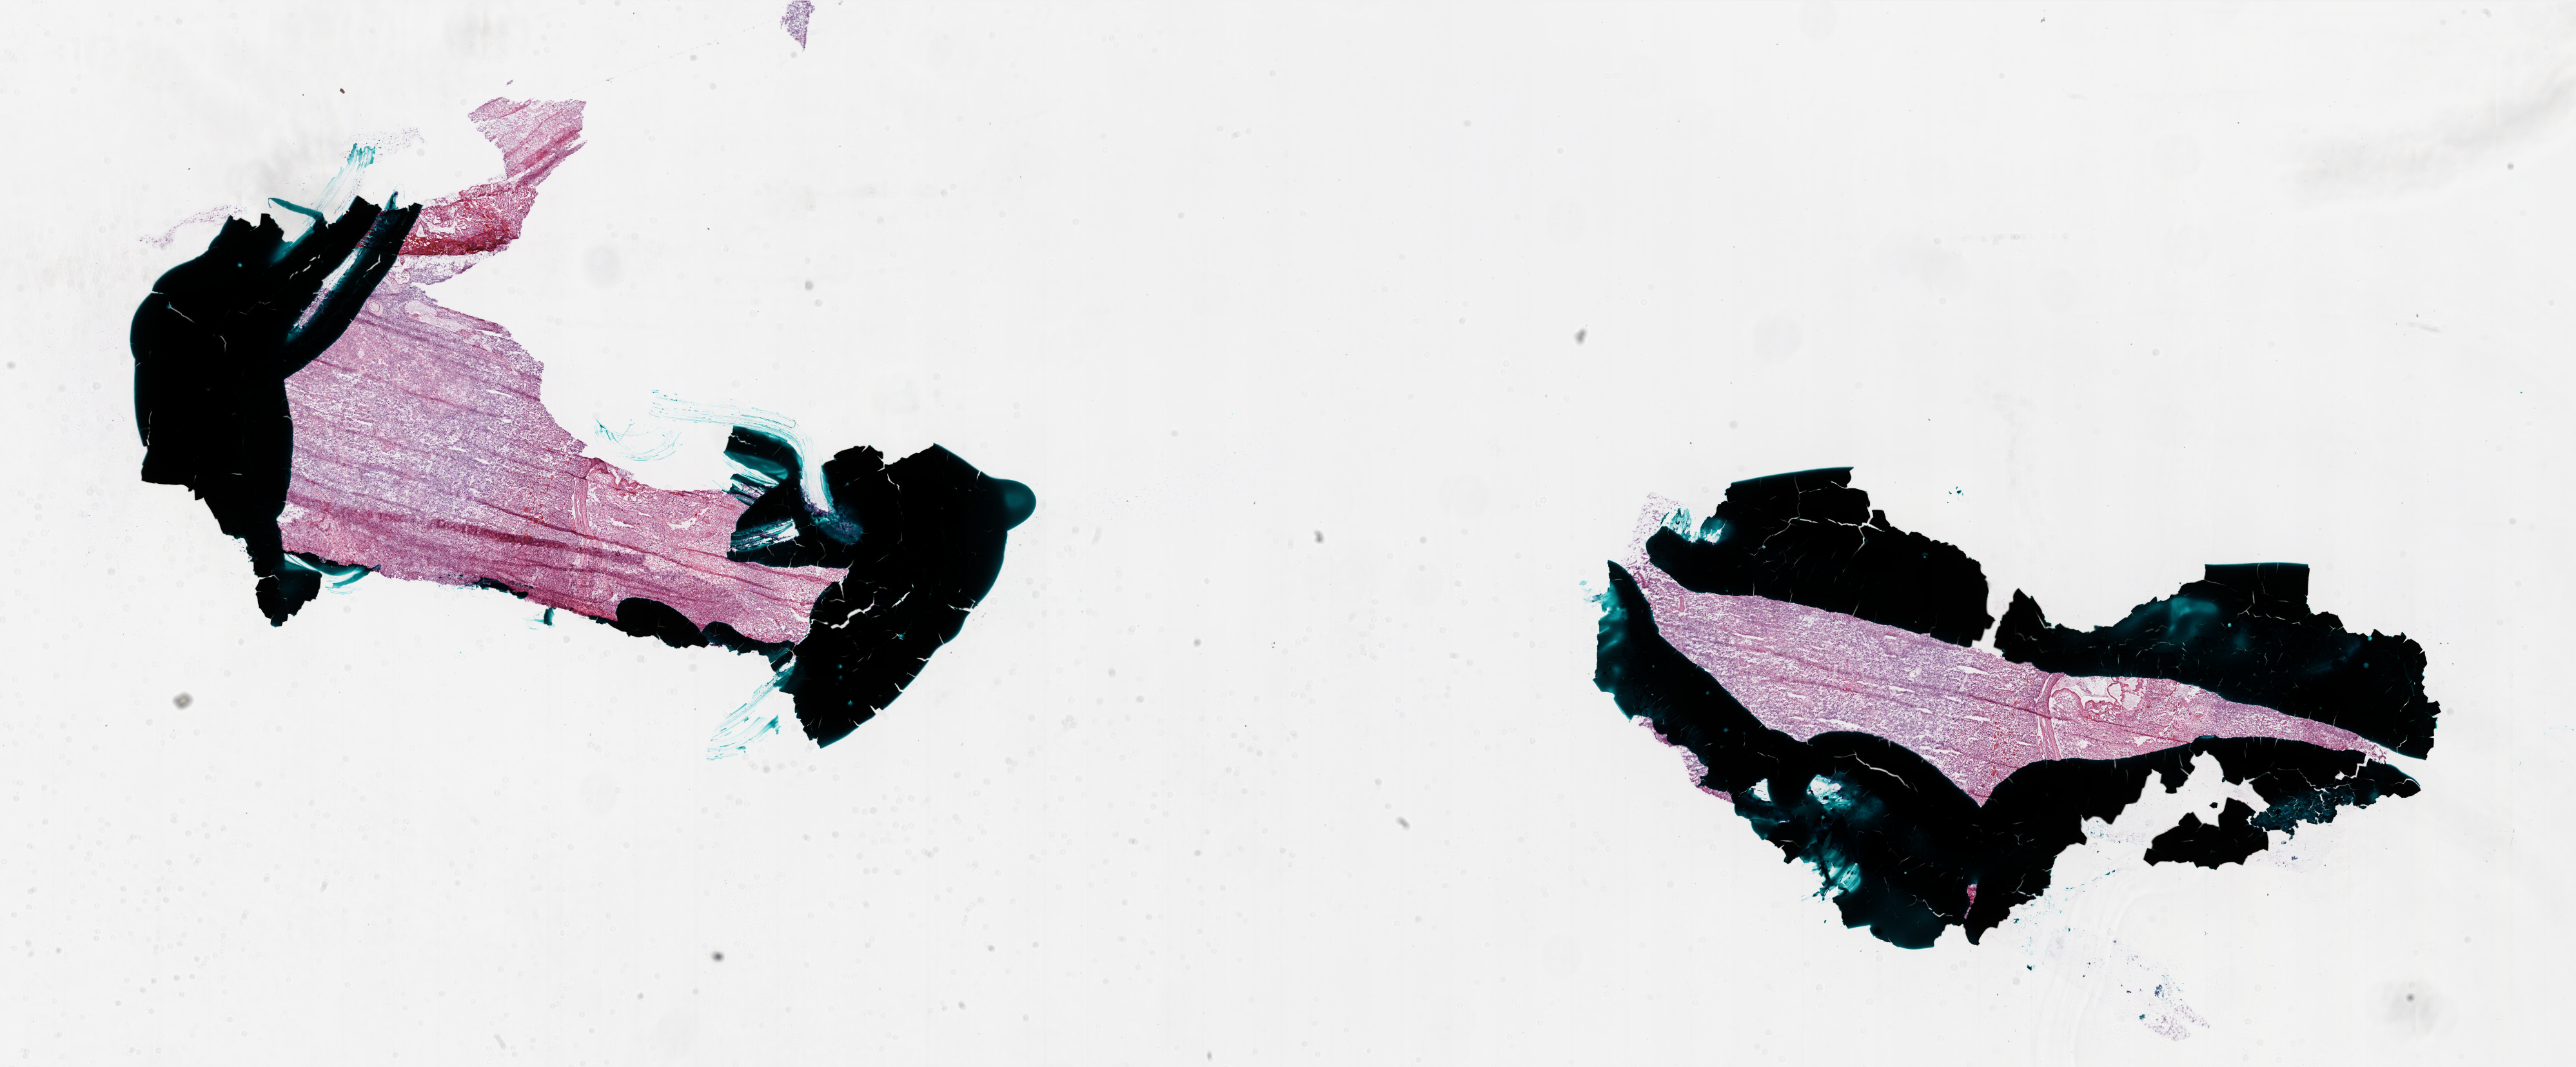
H&E-stained whole-slide image, a low-resolution overview of the entire scanned area, about 32.0 x 13.2 mm, frozen section, brain, primary tumour sample. Patient: male, age at initial diagnosis 54 years. Composition of this section per pathologist review: tumour cells 50%, tumour nuclei 100%, normal cells 0%, stromal cells 0%, necrosis 50%.
• diagnosis: Glioblastoma